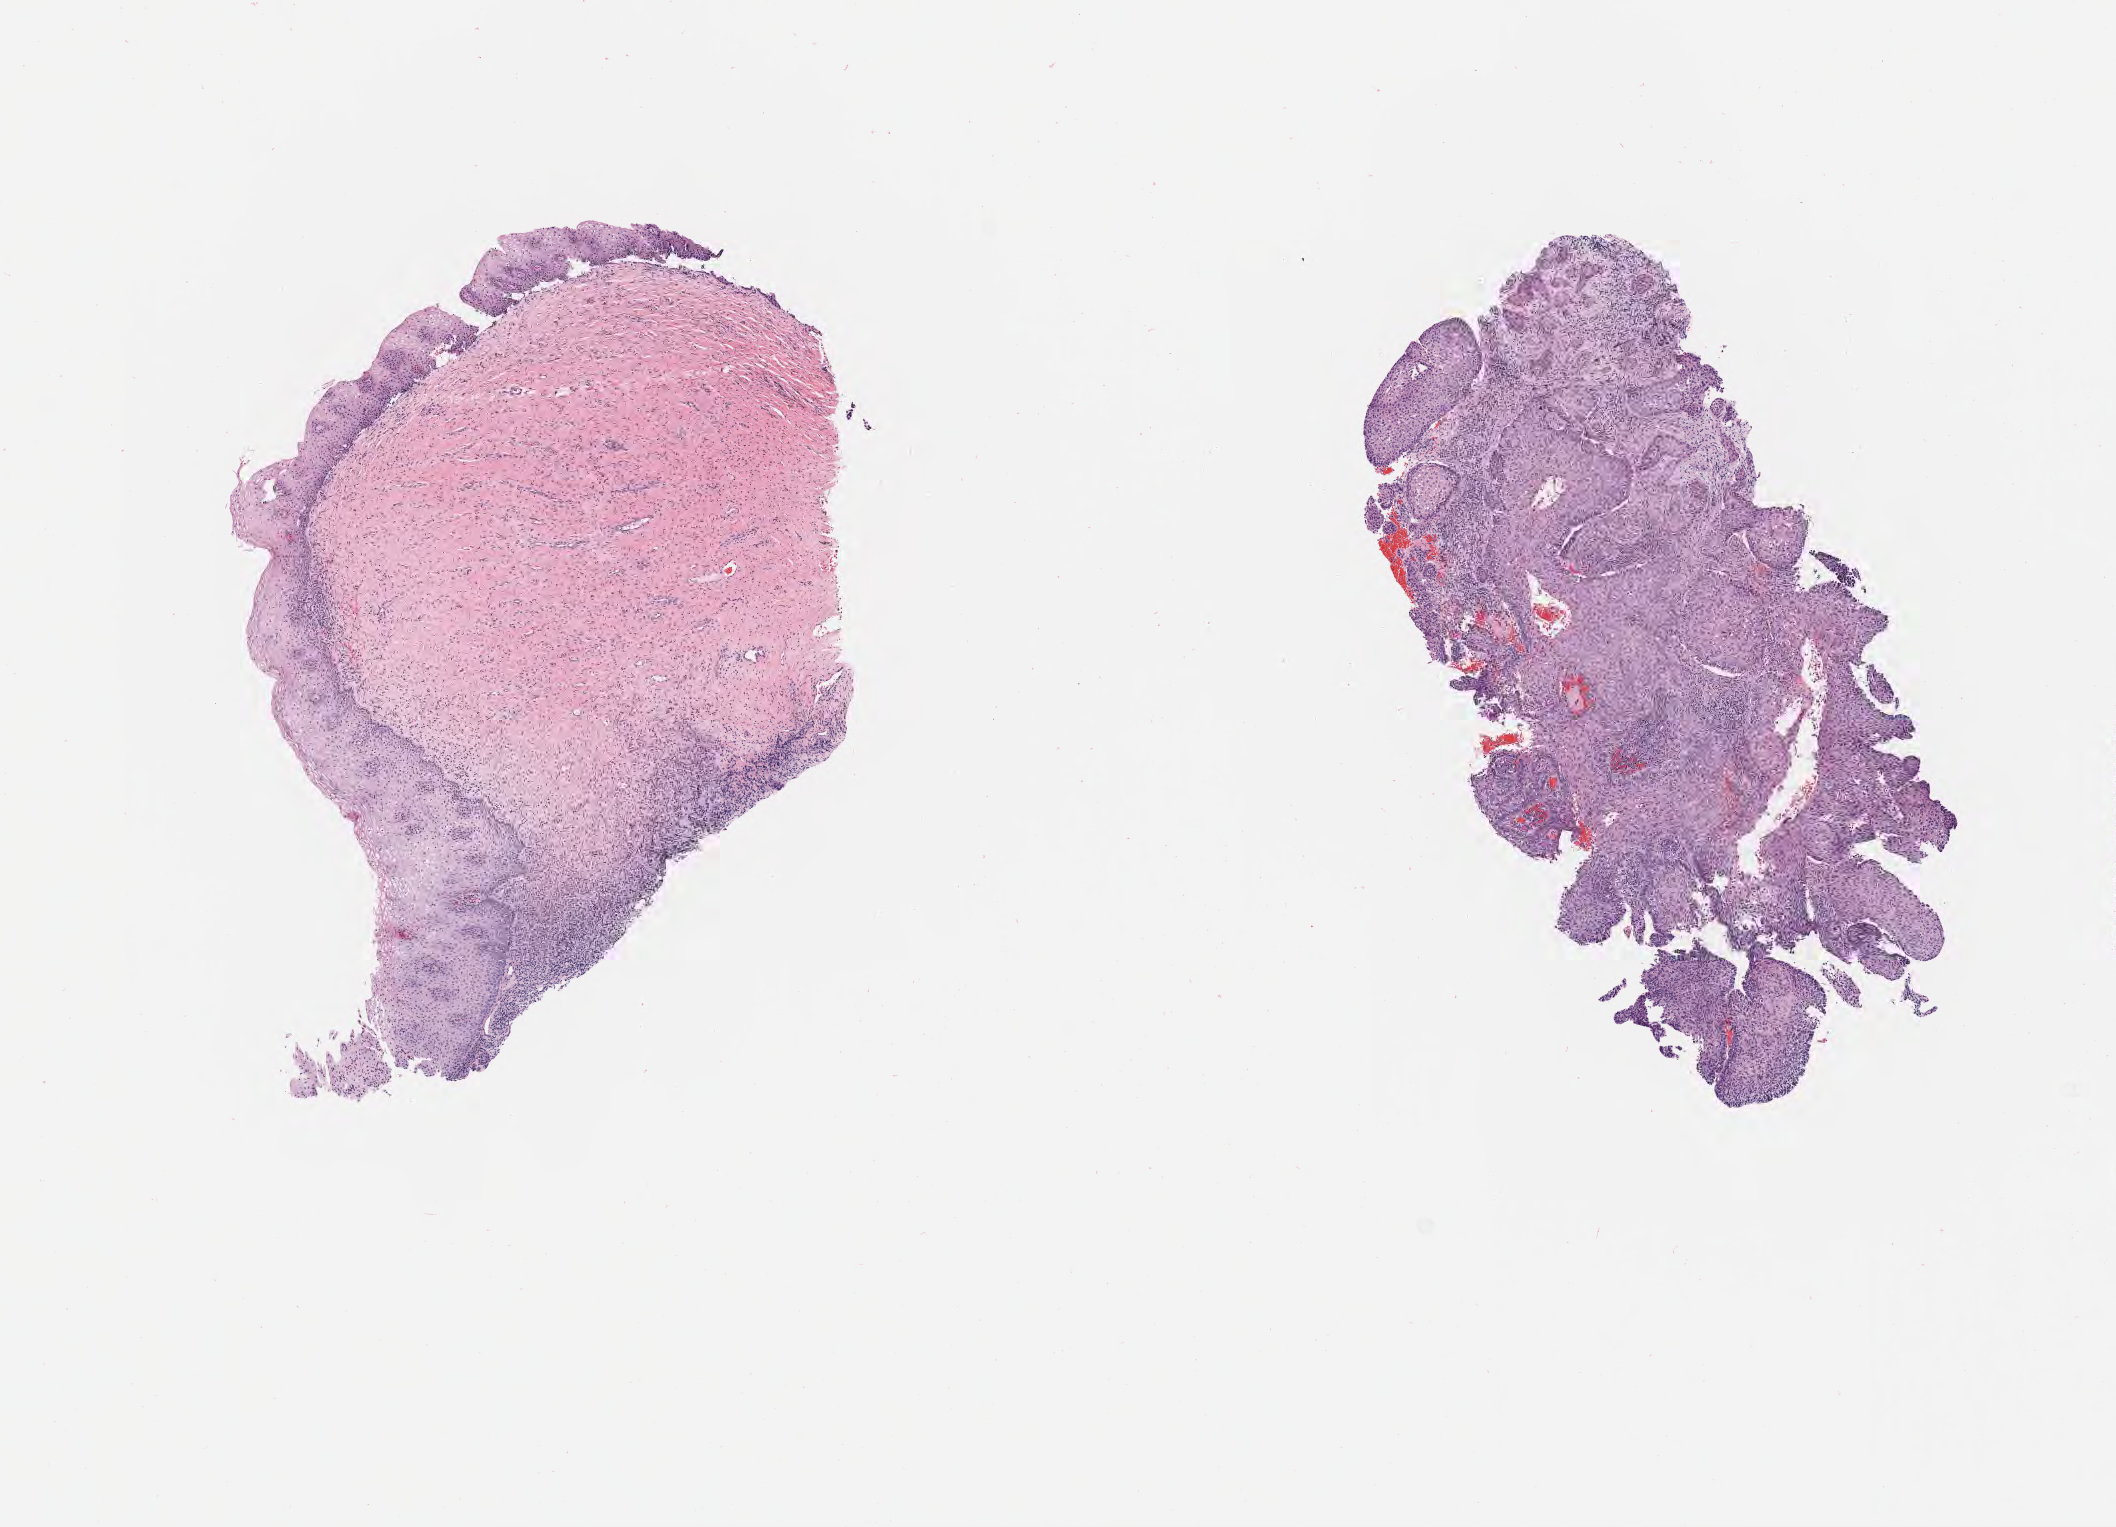
Digitized H&E-stained section — shown as a low-resolution overview of the whole scanned area (about 8.6 x 6.2 mm), specimen: tumor tissue, anatomic site: cervix. Patient: female, aged 40.
Histologic diagnosis: Squamous cell carcinoma, large cell, nonkeratinizing, NOS.